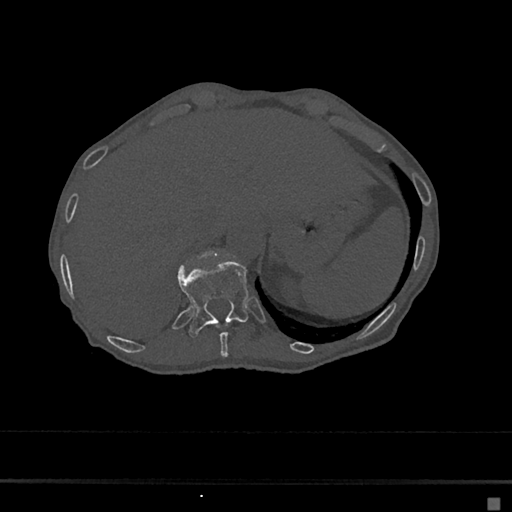
CT including the spine, one axial slice. Position 184 of 797 along the scan axis. Reconstruction kernel Br40s/3. Bone window (W 1800 / L 400 HU). 0.5 mm slice thickness. 512 × 512 image matrix. Female patient, age 68 years. From the clinical record (not read from this slice): primary cancer: renal.
Annotated regions visible in this slice (semi-automatic segmentation, software-assisted and operator-edited):
- T10 vertebra: bounding box <216,323,229,356> (left, top, right, bottom; pixels)
- T11 vertebra: <177,260,249,338>
- T12 vertebra: <202,253,207,258>